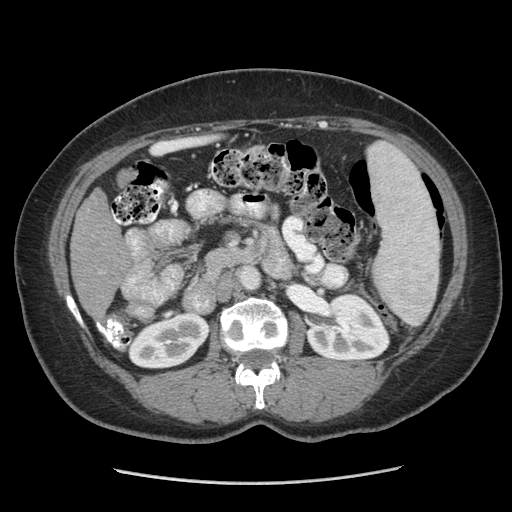
Contrast-enhanced abdominal CT (liver protocol), one axial slice. Slice 125 of 185 in the series (ordered by position). Reconstruction kernel STANDARD. Soft-tissue window (W 400 / L 40 HU). 2.5 mm slice thickness. 512 × 512 image matrix. From the clinical record (not read from this slice): diagnosis: hepatocellular carcinoma (patient treated with transarterial chemoembolisation; whether this scan precedes or follows treatment is not stated here); TNM stage (as recorded): Stage-I; Child-Pugh class: A; tumour nodularity: uninodular.
Annotated regions visible in this slice (semi-automatic segmentation, software-assisted and operator-edited):
- liver parenchyma outside the tumour (the mass and vessels are separate outlines, so this box may not span the whole liver): bounding box <70,188,132,309> (left, top, right, bottom; pixels)
- mass: <116,169,135,187>
- liver vessels: <115,218,119,222>